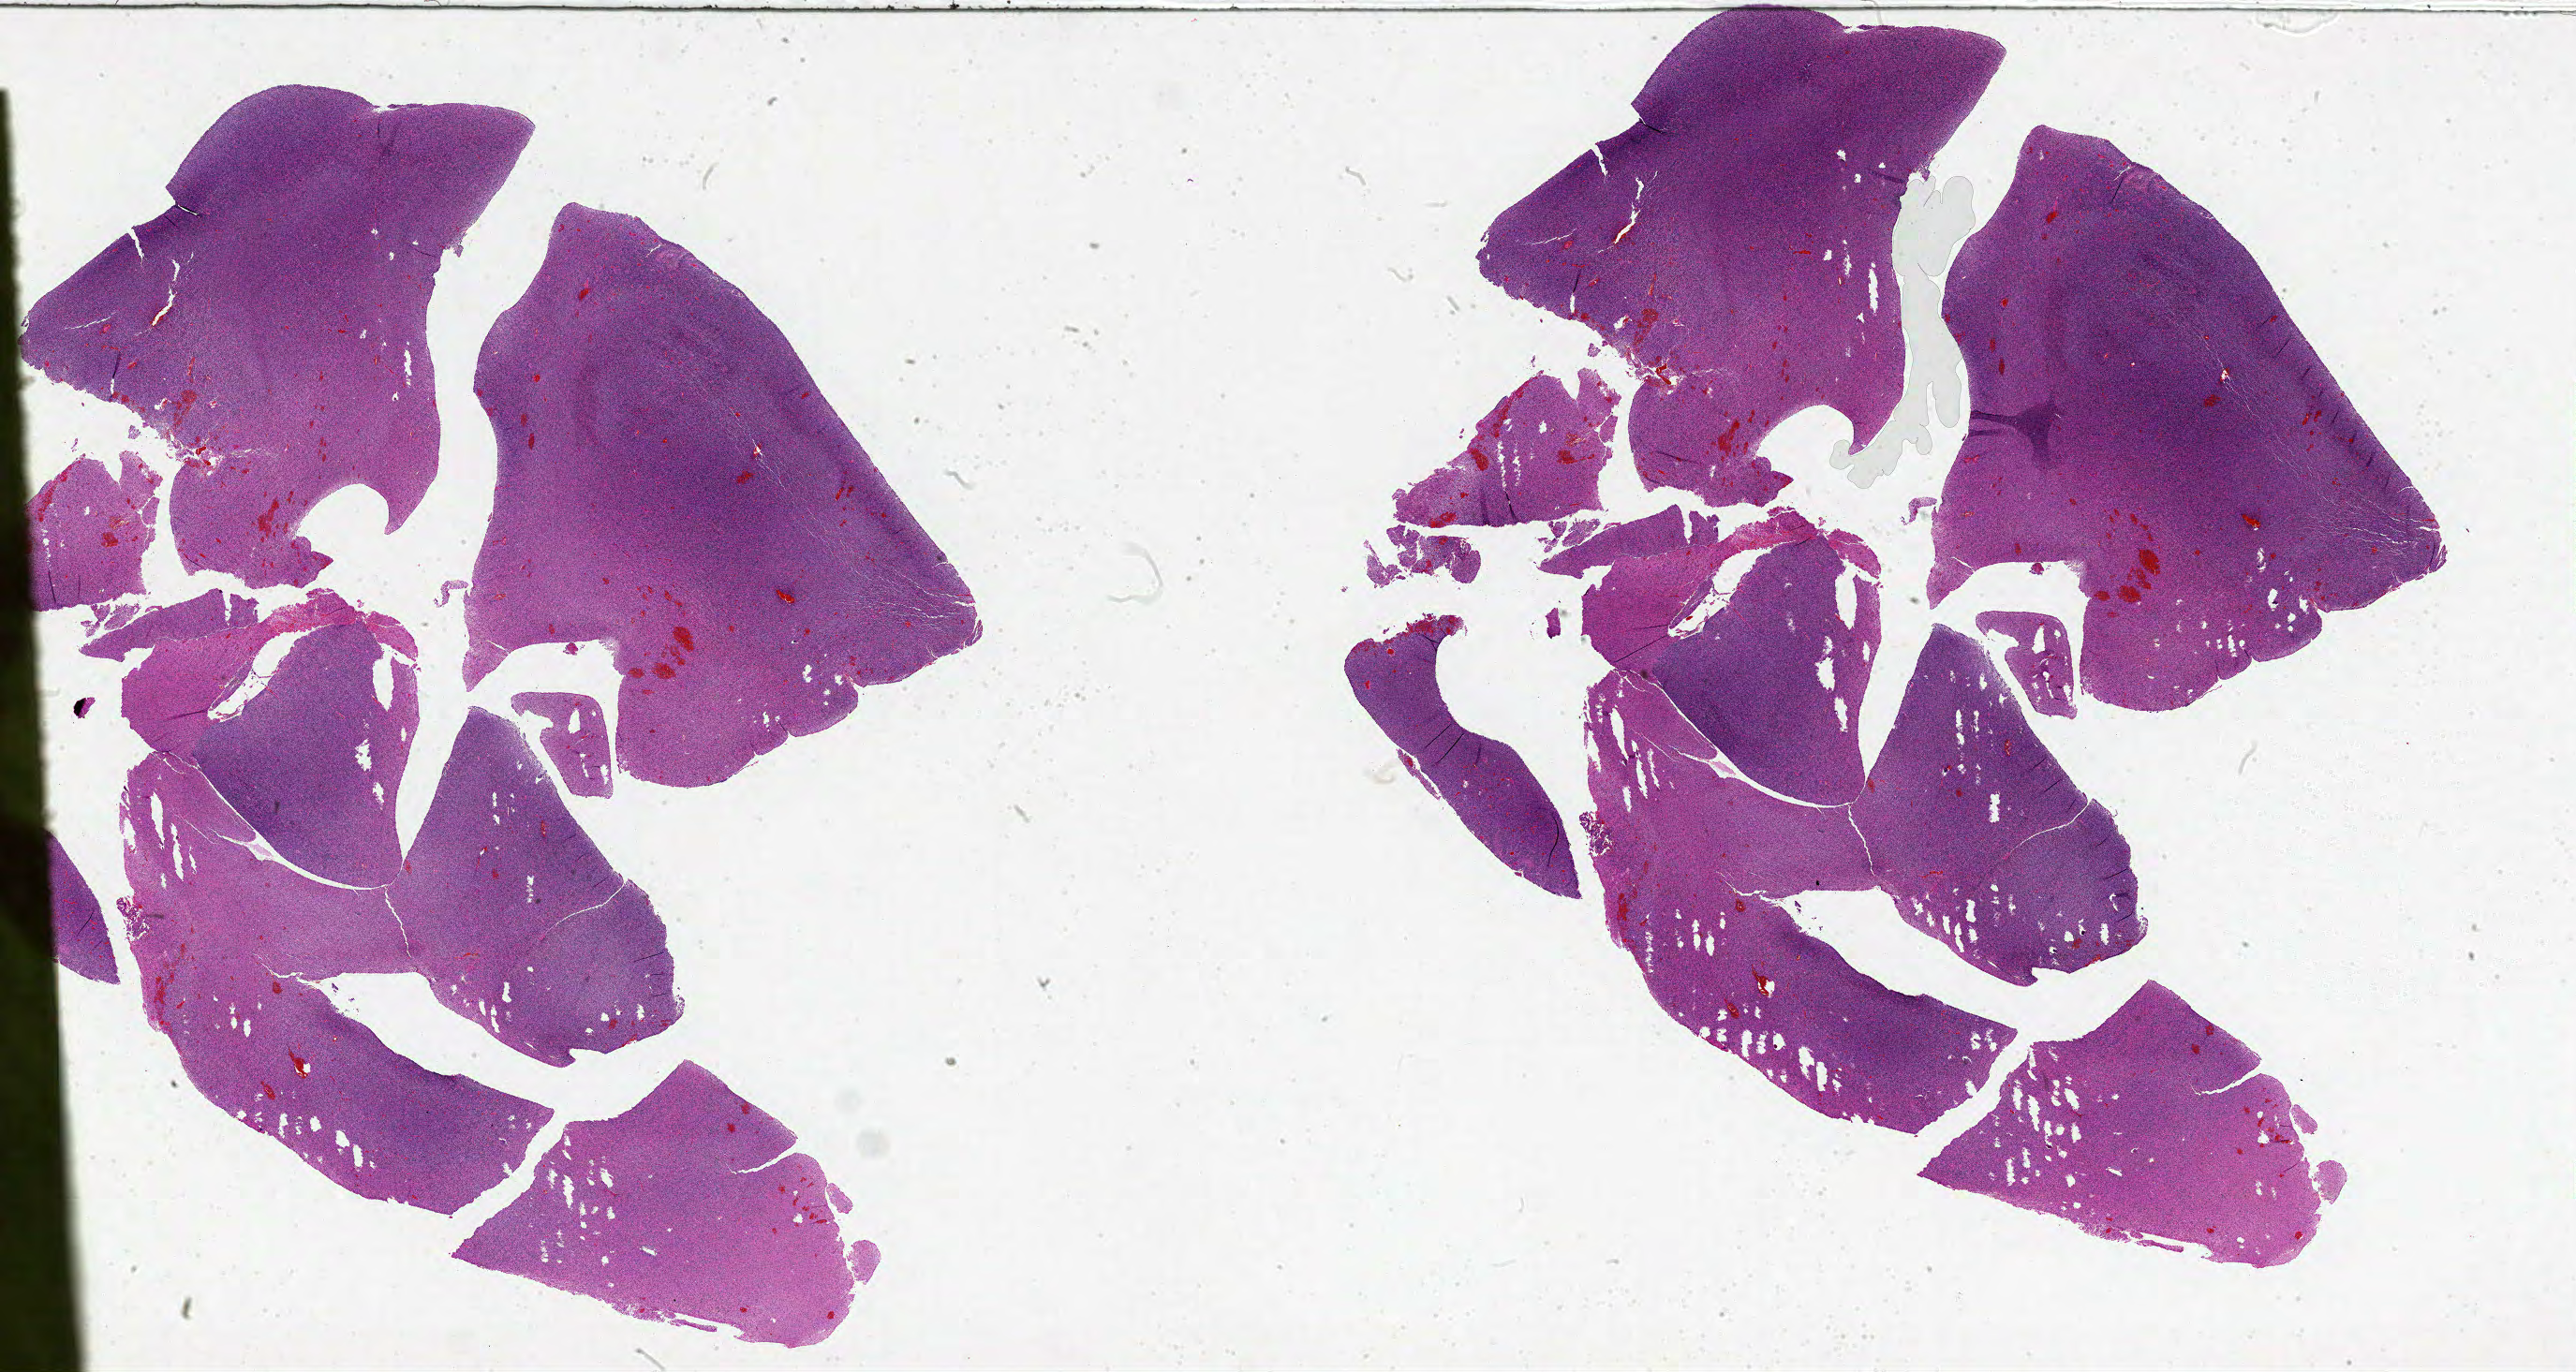
H&E whole-slide image — shown as a low-resolution overview of the whole scanned area (about 44.0 x 23.4 mm, acquisition: 20x scan). FFPE section. Brain, primary tumour sample. Patient: male, age at initial diagnosis 46 years.
Diagnosis: Glioblastoma.